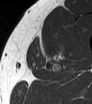
MRI of an extremity soft-tissue mass, one axial slice. Slice 45 of 62 in the series (ordered by position). MR volume resampled by the dataset authors to the PET/CT grid (not the native acquisition matrix). 3.27 mm slice thickness. 92 × 104 image matrix, field of view 90 × 102 mm. Male patient. Case-level facts recorded for this patient, not image findings: histological type: mixoid liposarcoma; grade: low; site of the primary tumour: left thigh.
Annotated regions visible in this slice (expert contour drawn on MRI and transferred to this co-registered scan by the dataset authors):
- gross tumour volume (mass): box from (x=41, y=41) to (x=63, y=62) px